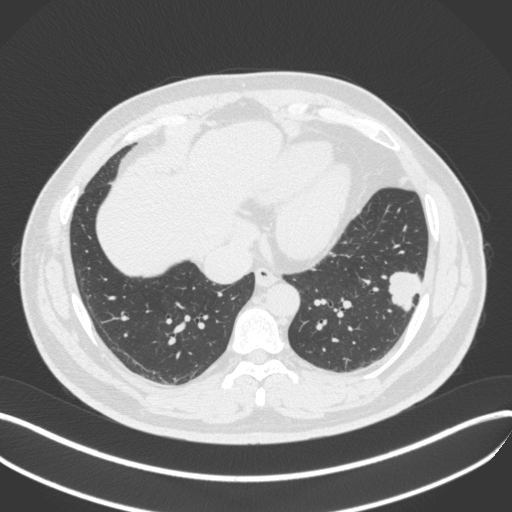
Chest CT, one axial slice; position 135 of 420 along the scan axis; lung window (W 1500 / L -600 HU); 1 mm slice thickness; 512 × 512 image matrix. Male patient, age 39 years. Case-level facts recorded for this patient, not image findings: clinical TNM (as recorded): T2a N0 M0.
Structures marked on this image (bounding box drawn by a radiologist):
- lung tumour (recorded histology: adenocarcinoma): box from (x=383, y=262) to (x=426, y=311) px